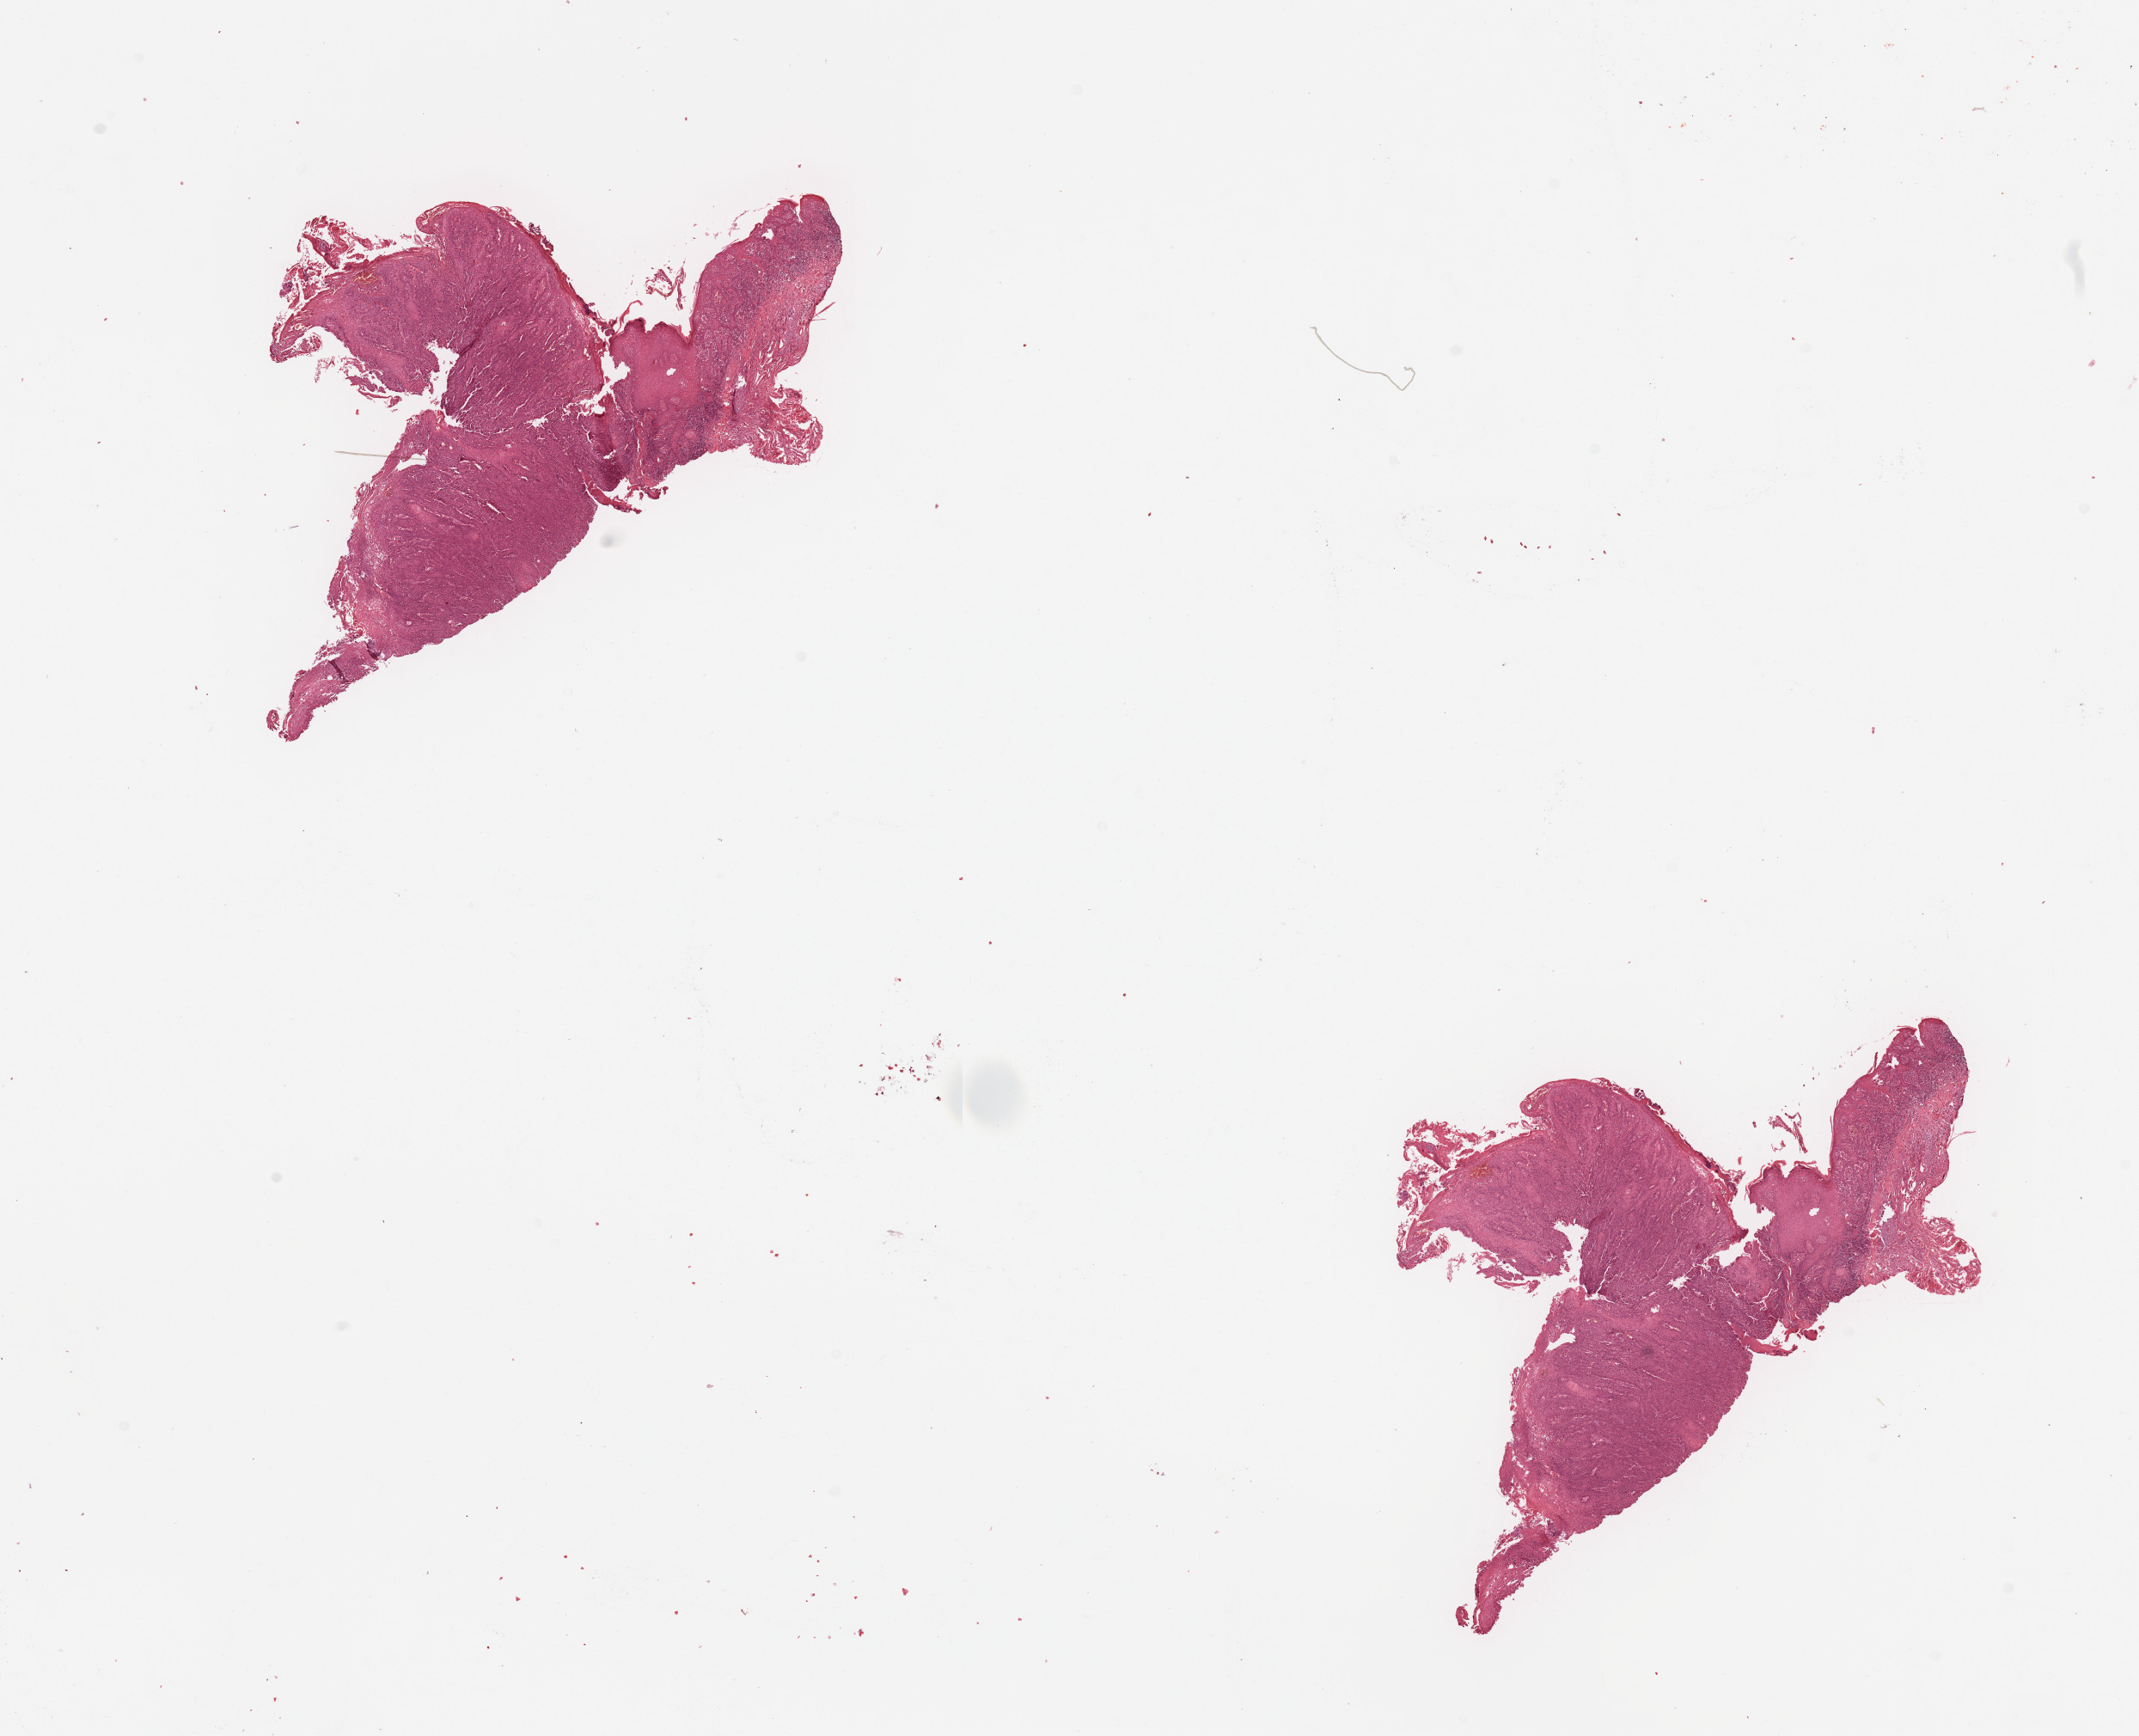
Digitized H&E-stained tissue section (whole slide) — low-resolution overview of the scanned area, about 19.7 x 16.0 mm (acquisition: 20x scan). Tumour tissue sample, sampled site: lip. Patient: male, age 76 years. Histologic grade: G1 (well differentiated). Composition of this section per pathologist review: tumour nuclei 90%, necrosis 0%.
AJCC pathologic stage: I. Diagnosis: Squamous cell carcinoma, NOS (lip, NOS). Primary tumour site (as recorded): lip.